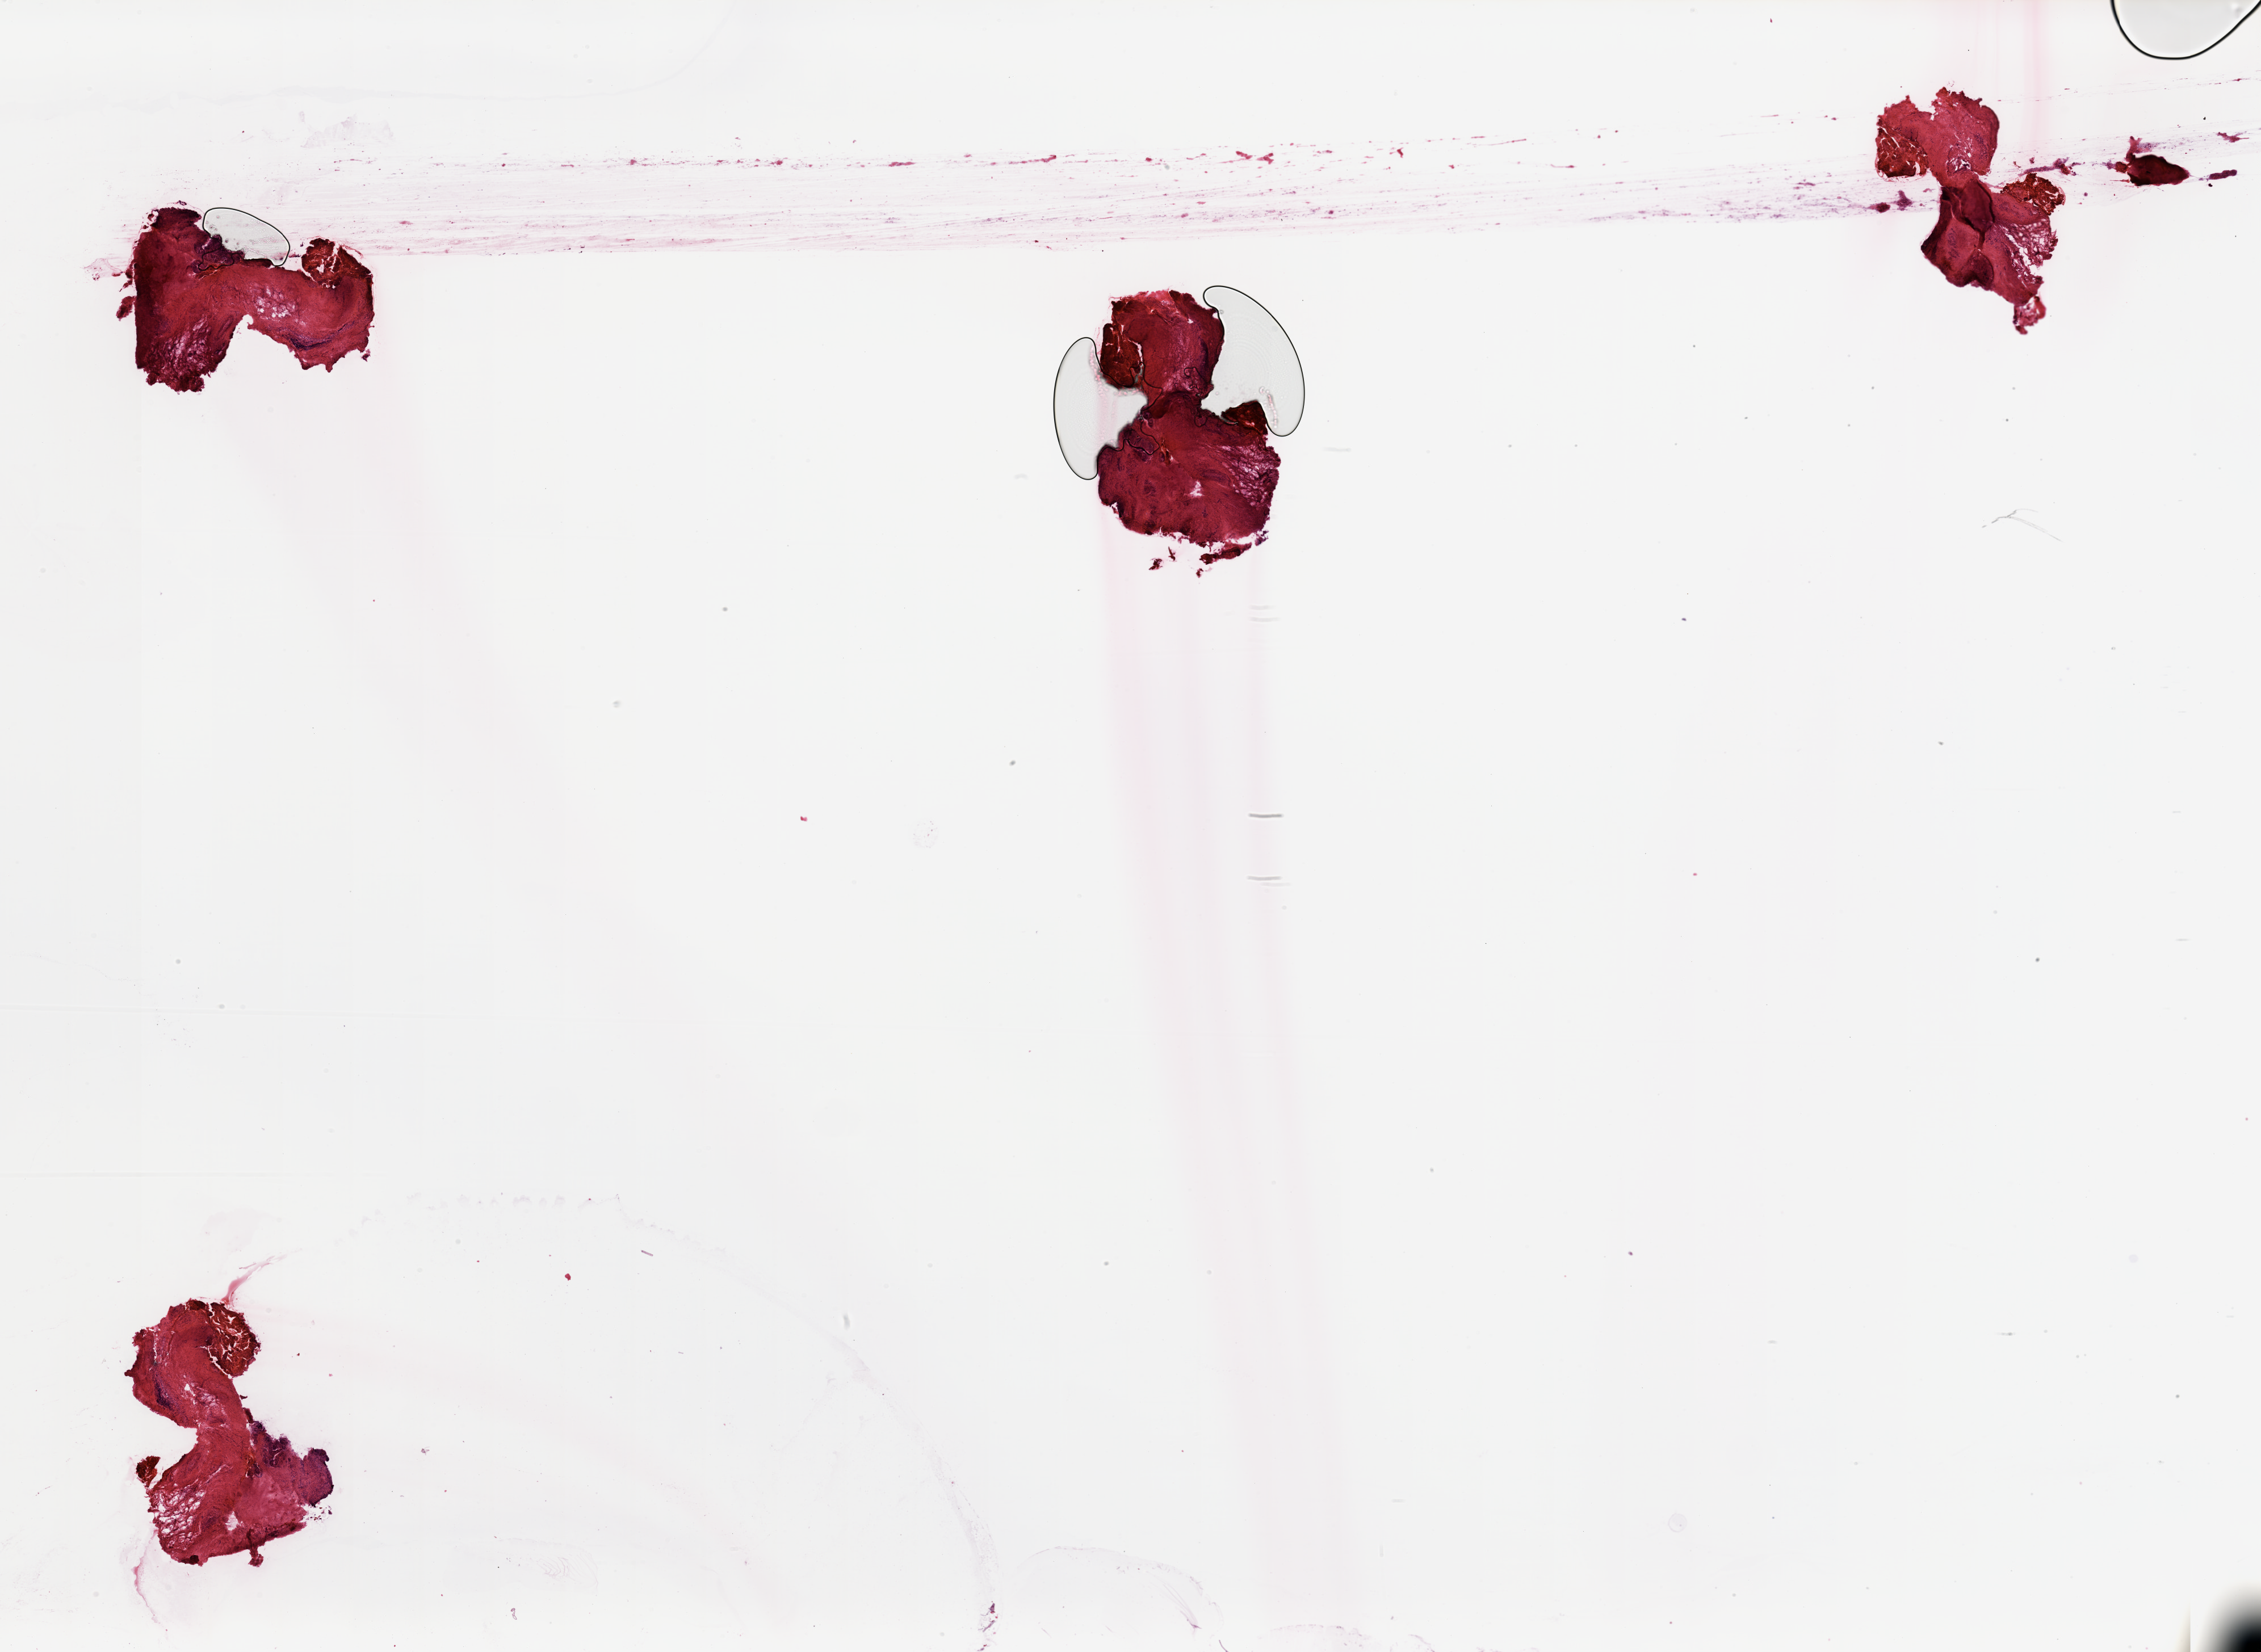
Digitized Hematoxylin and eosin (H&E) stained tissue section (whole slide) — whole scanned area (about 31.5 x 23.0 mm) shown as a low-resolution overview. Head and neck, tissue type not recorded. Male, 69 y/o.
Patient diagnosis: Squamous cell carcinoma, NOS (larynx, NOS).